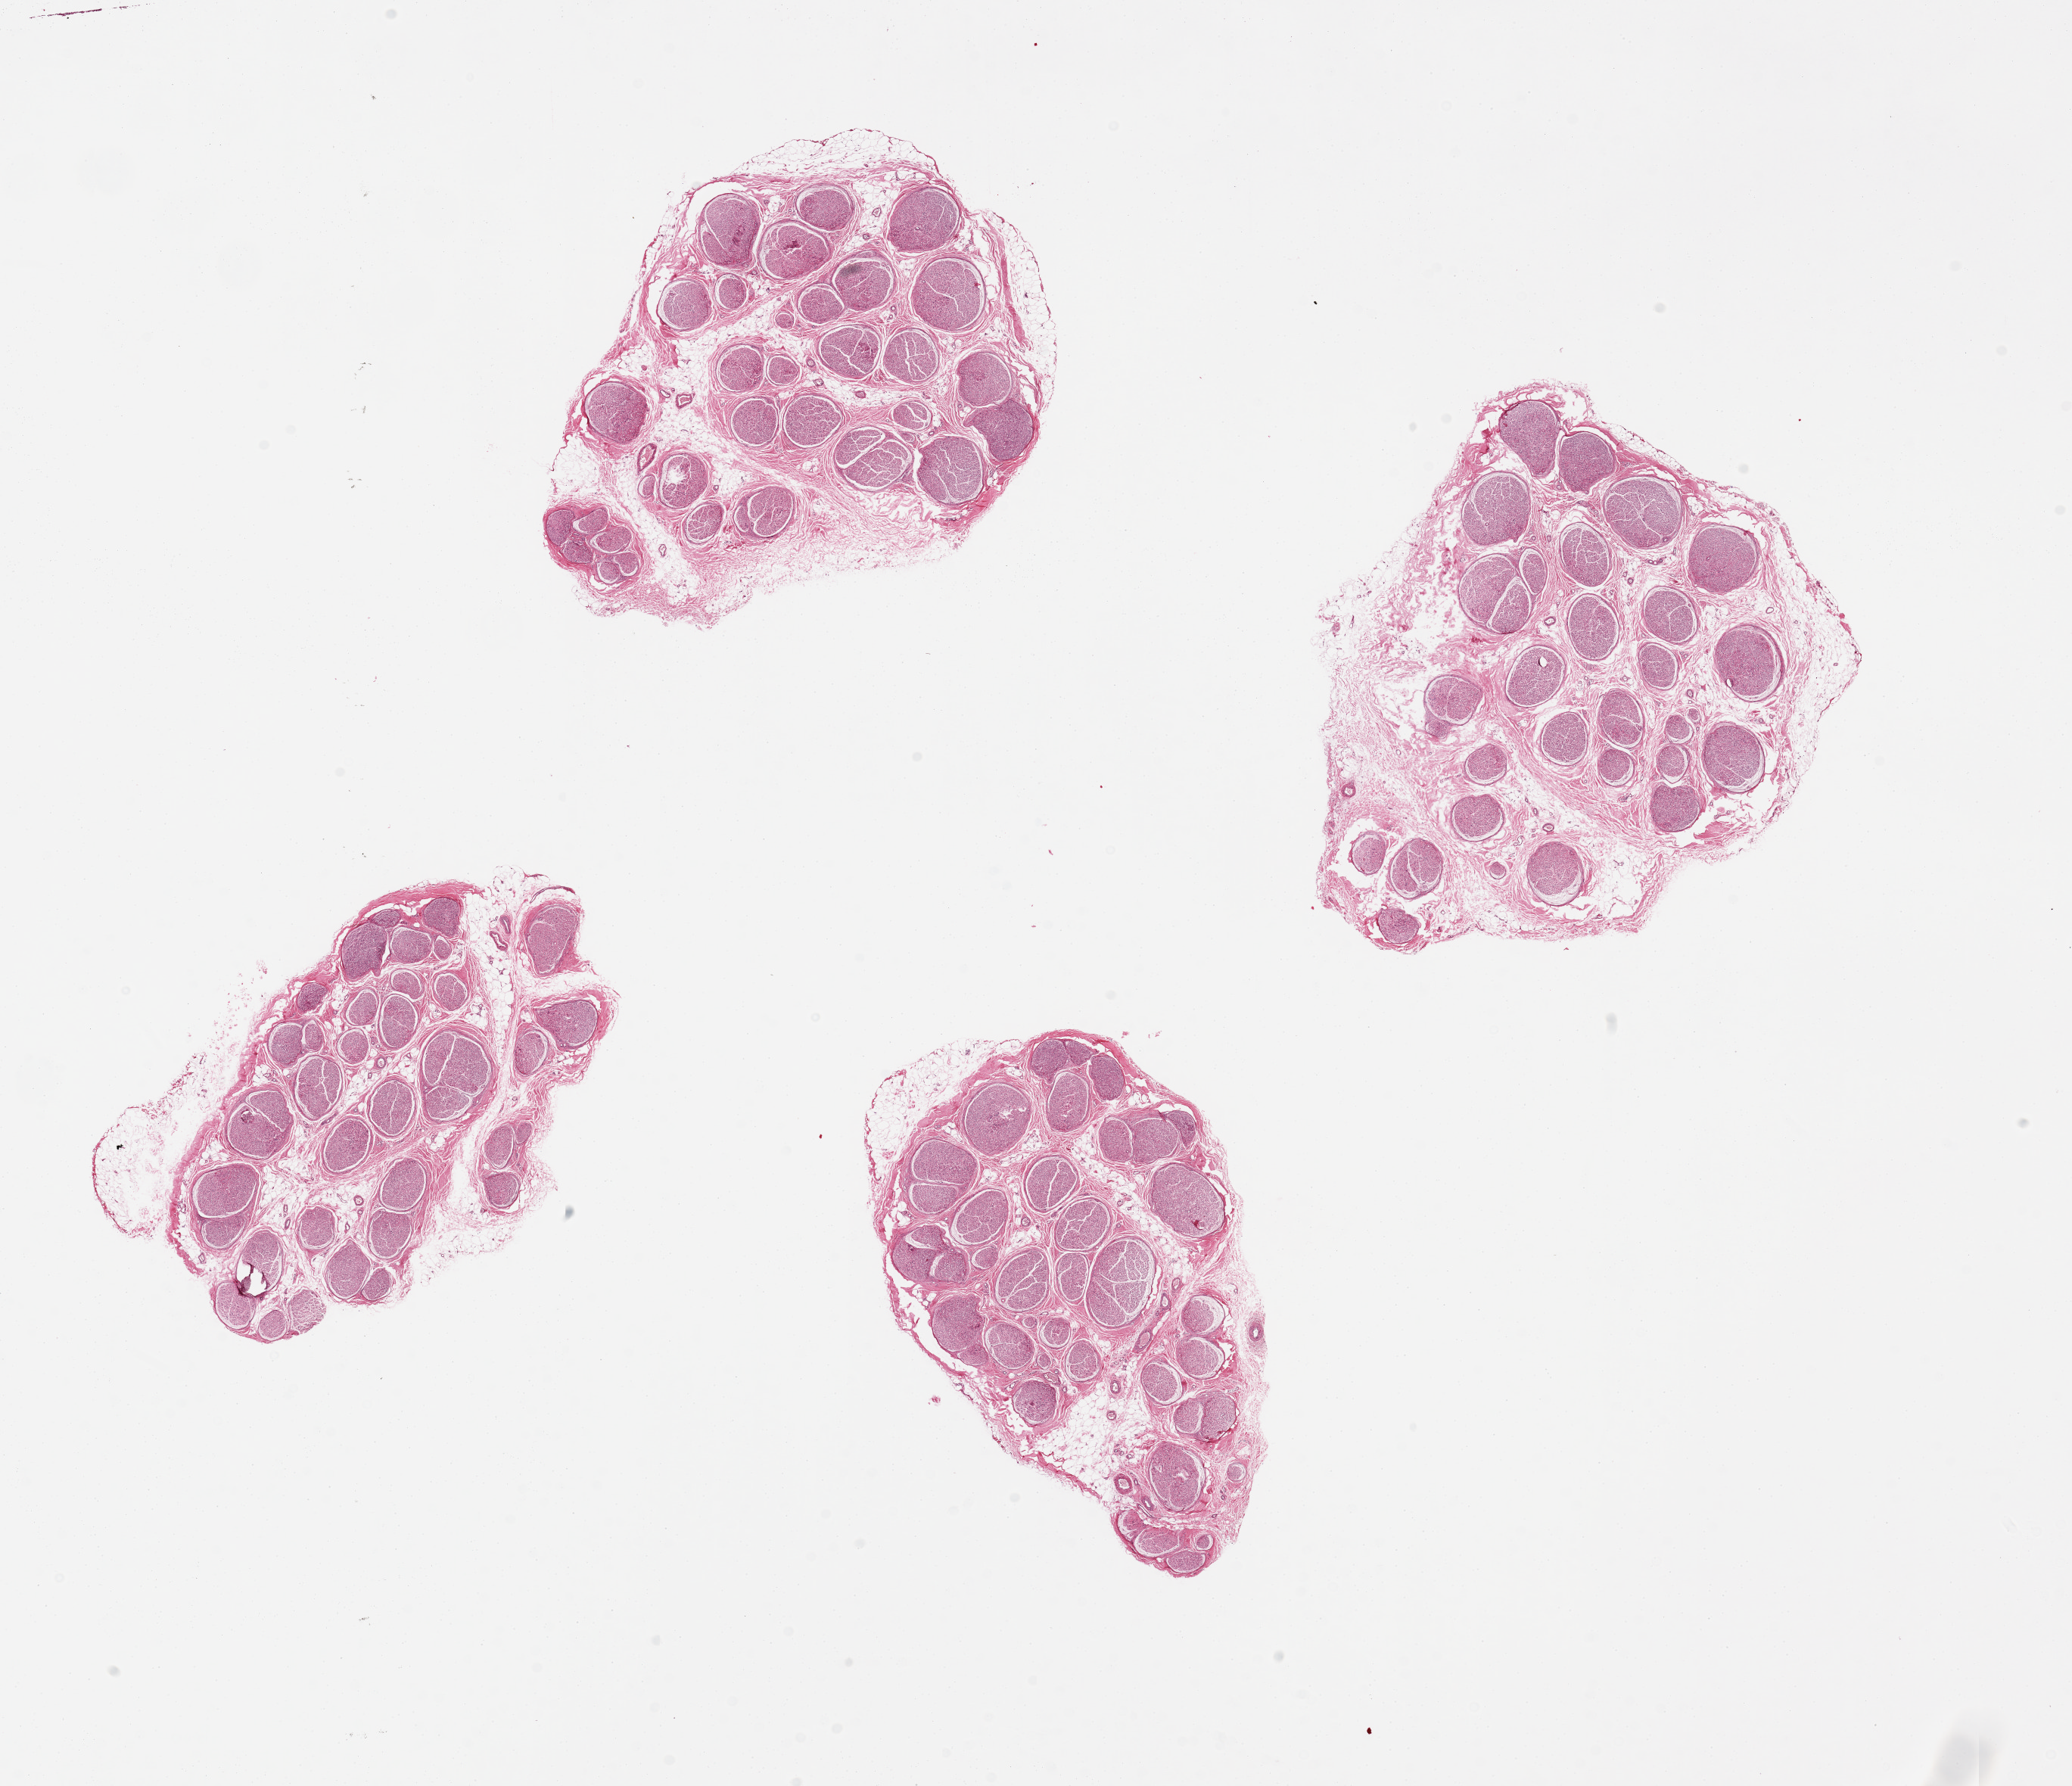
Whole-slide image, hematoxylin and eosin (H&E) stain — shown as a low-resolution overview of the whole scanned area (about 21.7 x 18.7 mm, slide scanned at 20x); PAXgene-fixed, paraffin-embedded tissue; target tissue: tibial nerve; donor tissue sample. Donor sex: female.
- review note (as recorded): 4 pieces, up to 6x5mm; good clean specimens